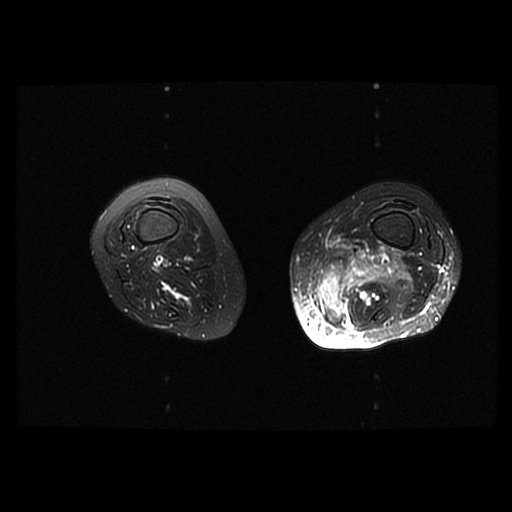
MRI of an extremity soft-tissue mass, one axial slice; position 20 of 42 along the scan axis; T2-weighted fat-saturated; 6 mm slice thickness; 512 × 512 image matrix. Female patient. From the clinical record (not read from this slice): histological type: pleomorphic leiomyosarcoma; grade: high; site of the primary tumour: left thigh.
Annotated regions visible in this slice (expert manual segmentation):
- gross tumour volume including surrounding oedema: bounding box (x1, y1, x2, y2) in pixels: (310, 244, 409, 330)